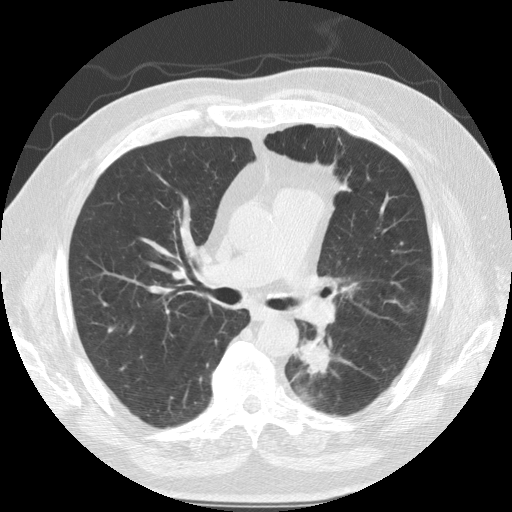
Low-dose screening chest CT, one axial slice. Slice 72 of 124 in the series (ordered by position). Reconstruction kernel STANDARD. 120 kVp. Lung window (W 1500 / L -600 HU). 2.5 mm slice thickness. 512 × 512 image matrix.
Annotated regions visible in this slice (manually delineated by an expert):
- lesion 1 (tumor, lower lobe of left lung): bounding box (x1, y1, x2, y2) in pixels: (293, 339, 335, 378)